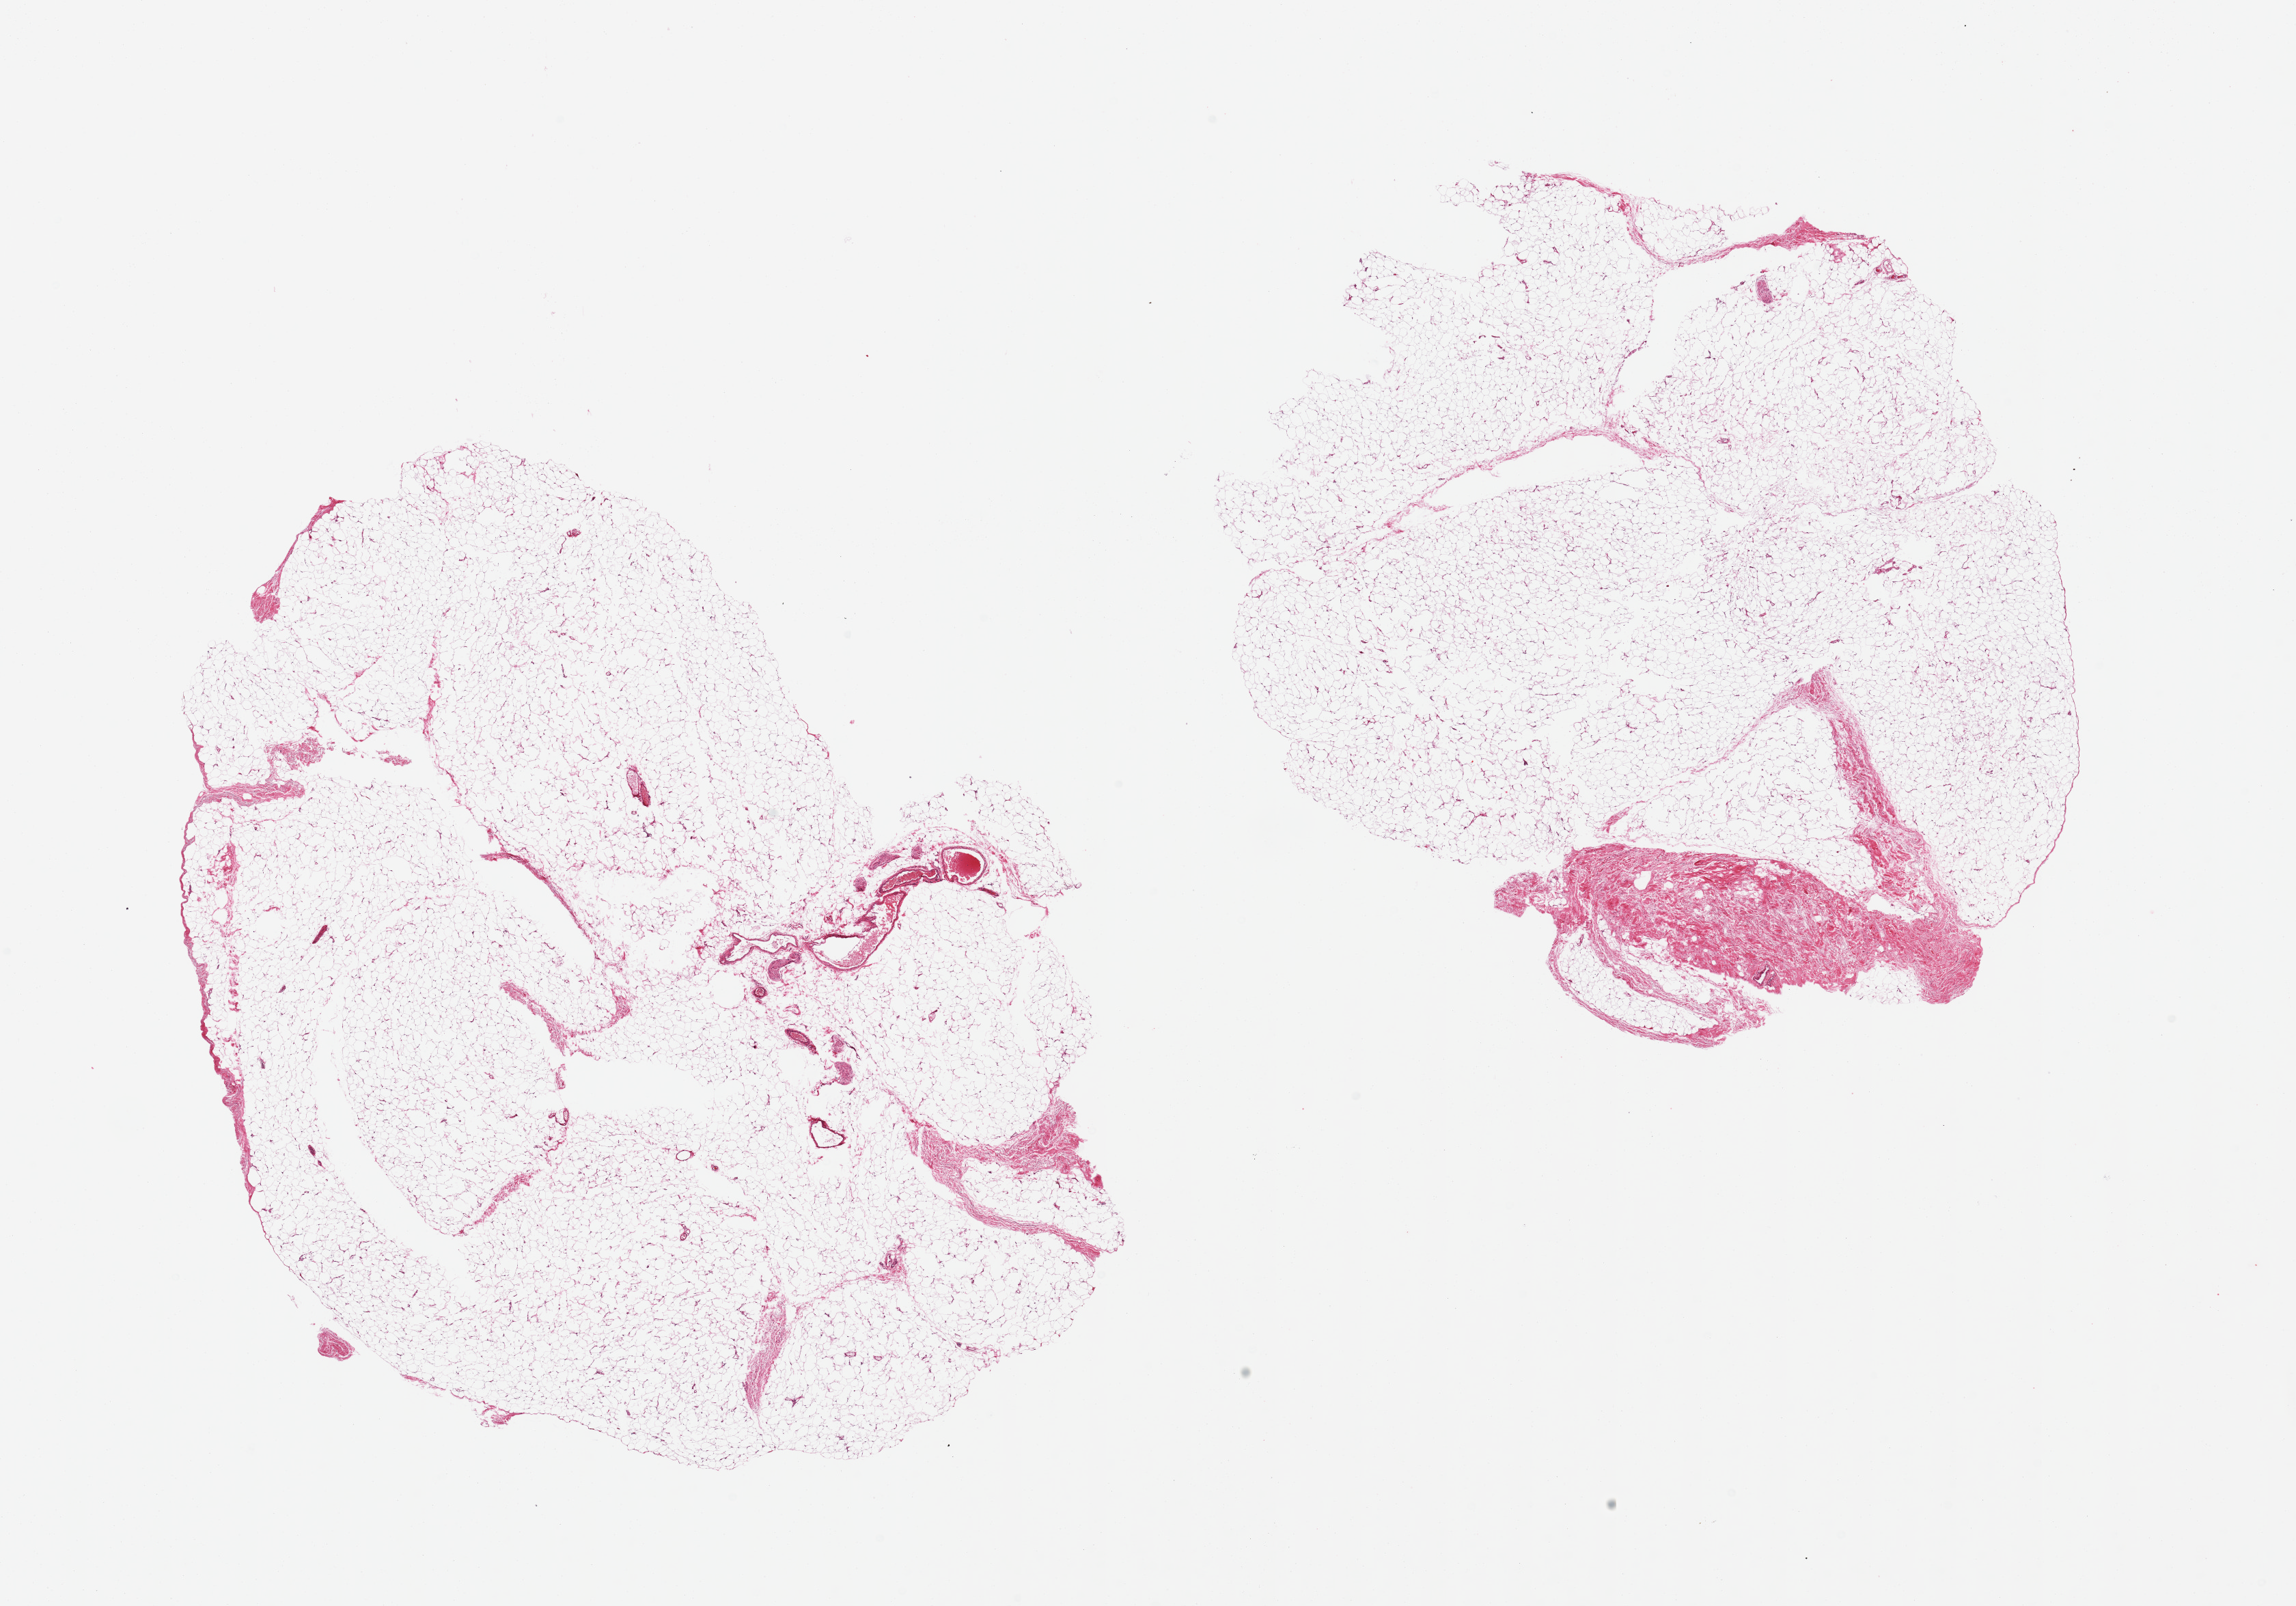
Digitized H&E-stained section, whole scanned area (about 26.6 x 18.6 mm) shown as a low-resolution overview, PAXgene-fixed, paraffin-embedded tissue, section of adipose tissue (target tissue), tissue donor sample. Donor sex: female.
• review note (as recorded): 2 pieces, ~10% fascia/ vascular elements